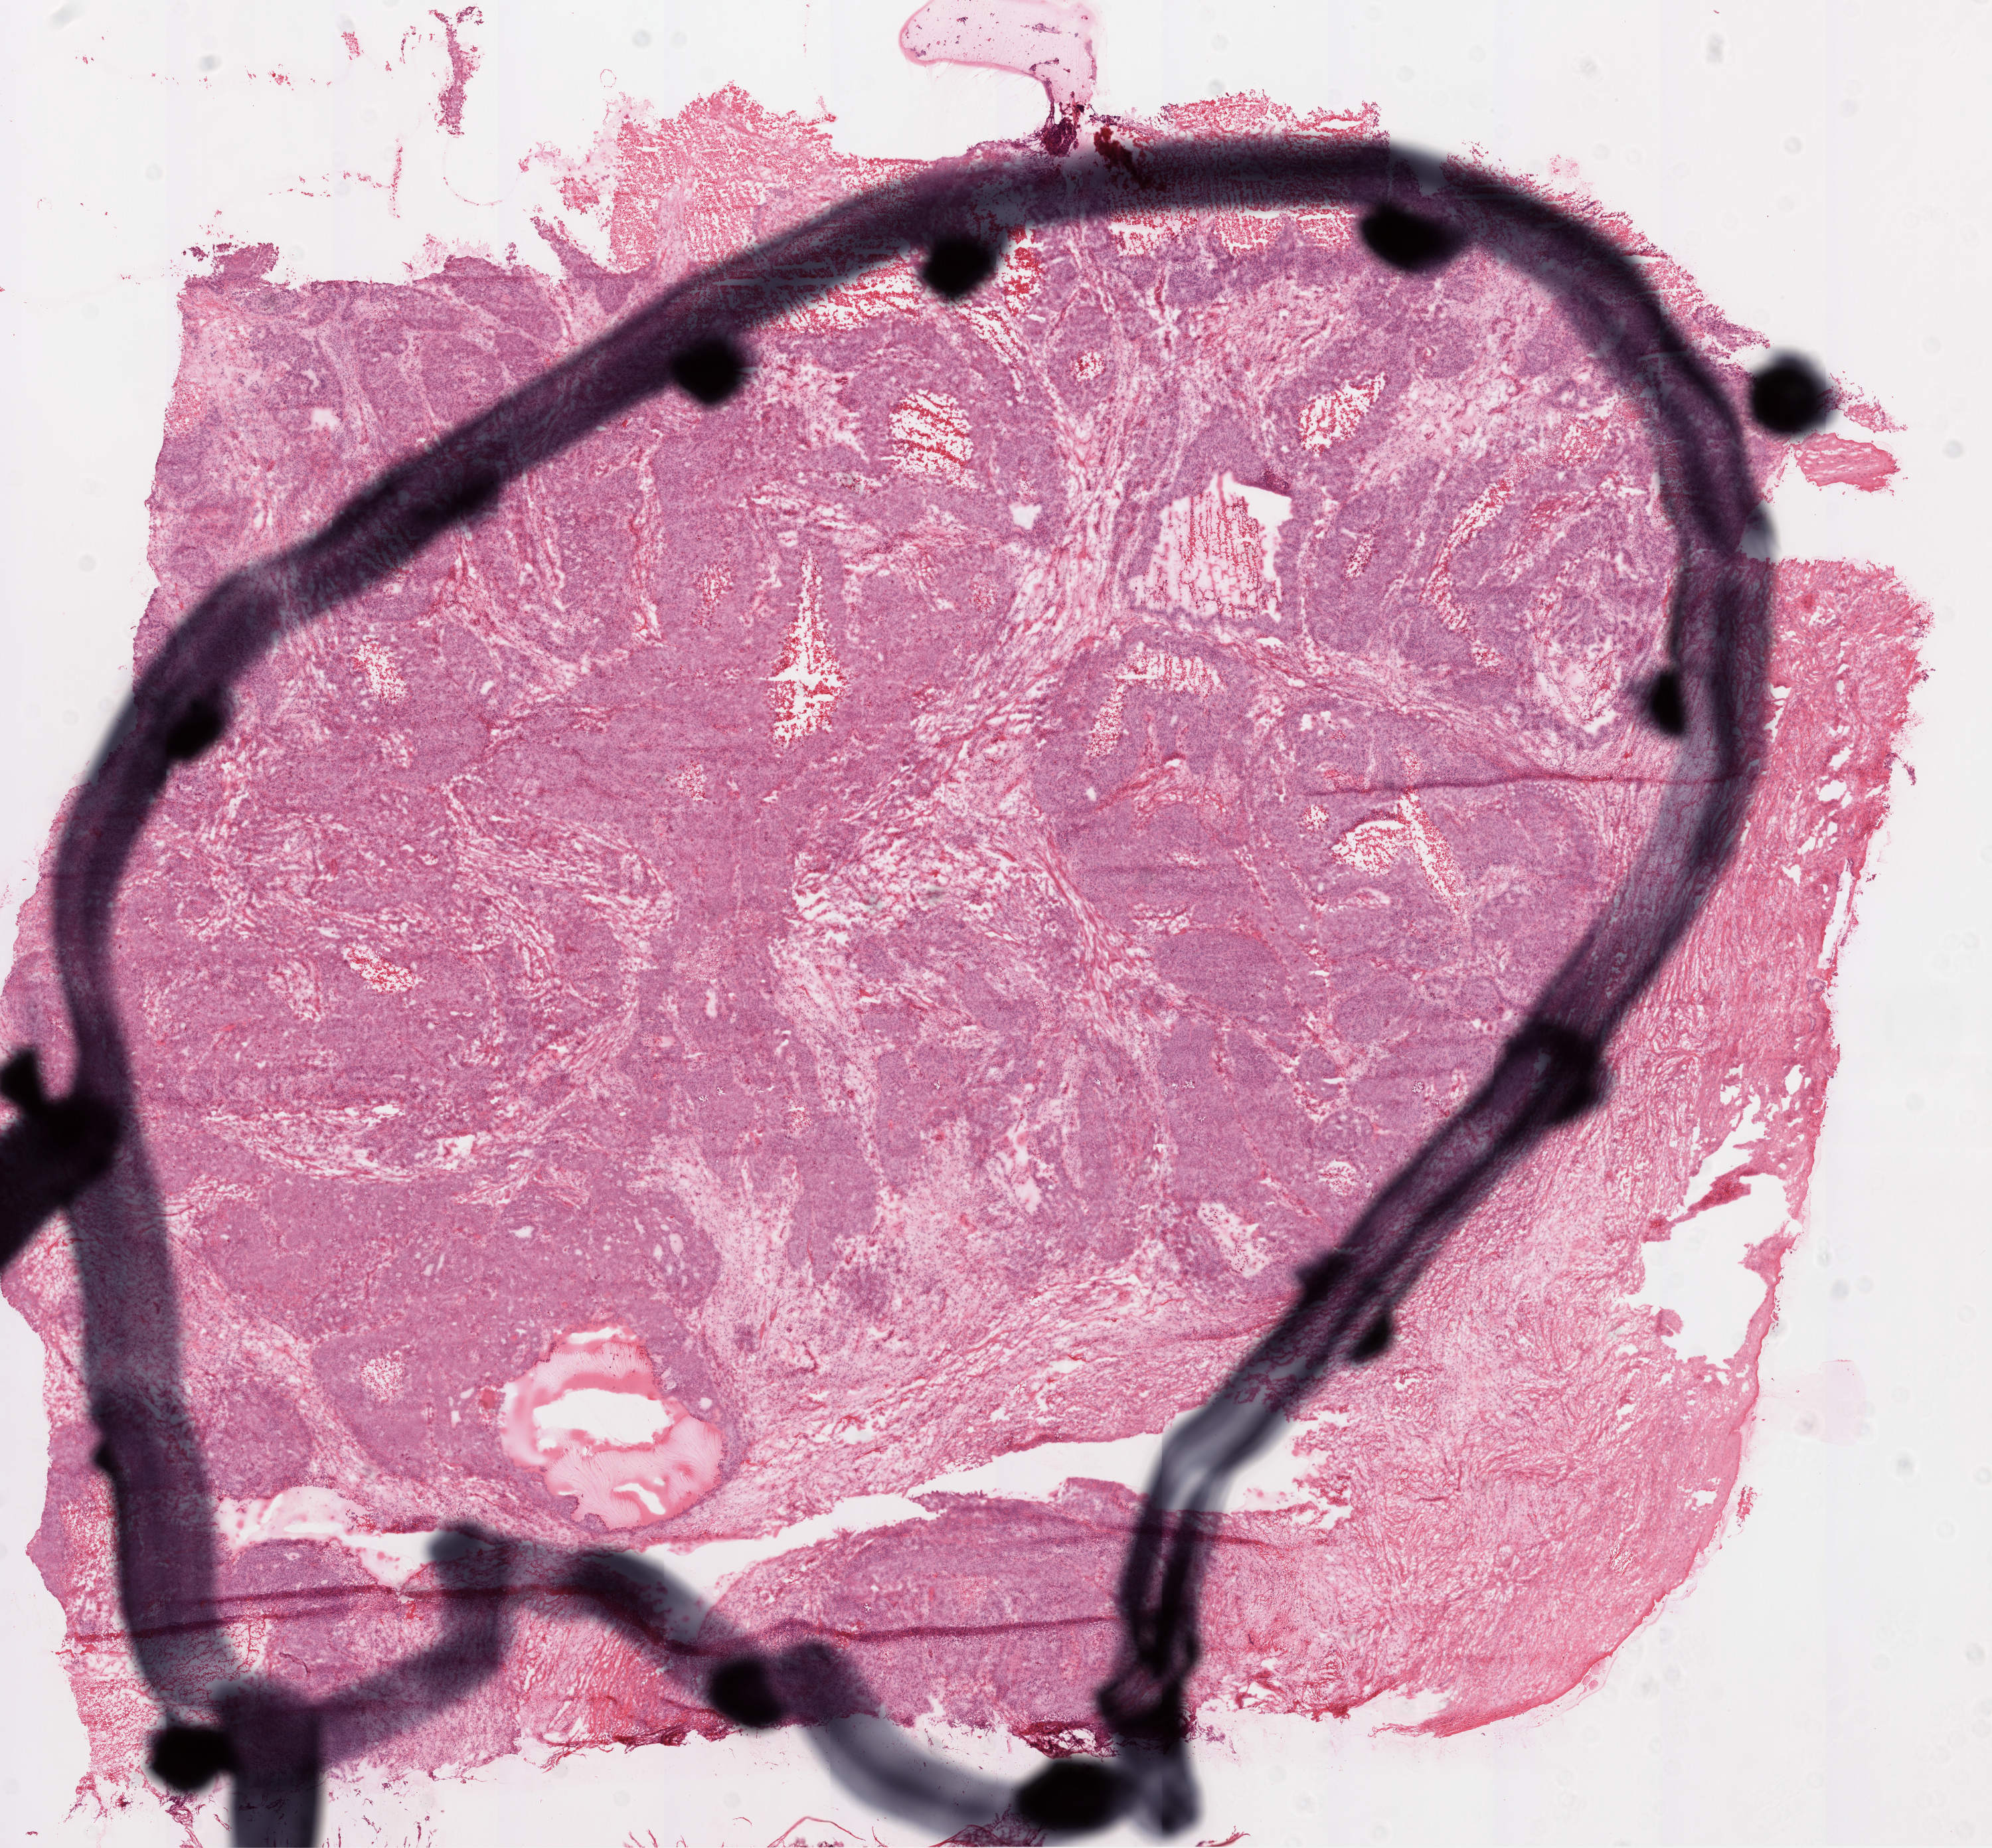
Whole-slide histology image, H&E-stained, whole scanned area (about 12.0 x 11.2 mm) shown as a low-resolution overview. Frozen section. Ovary, primary tumour sample. Female patient. Histologic grade: G3 (poorly differentiated). Composition of this section per pathologist review: tumour cells 80%, tumour nuclei 95%, normal cells 0%, stromal cells 20%, necrosis 0%.
* FIGO stage: IB
* diagnosis: Serous cystadenocarcinoma, NOS